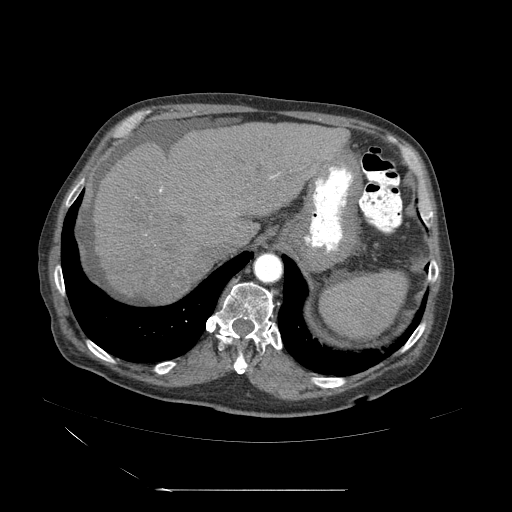
Contrast-enhanced abdominal CT (liver protocol), one axial slice. Slice 42 of 71 in the series (ordered by position). Reconstruction kernel STANDARD. 120 kVp. Soft-tissue window (W 400 / L 40 HU). 512 × 512 image matrix, field of view 440 × 440 mm. From the clinical record (not read from this slice): diagnosis: hepatocellular carcinoma (patient treated with transarterial chemoembolisation; whether this scan precedes or follows treatment is not stated here); TNM stage (as recorded): Stage-II; Child-Pugh class: A; tumour nodularity: multinodular; tumour size: 1 cm.
Outlined on this slice (semi-automatically segmented with operator editing):
- abdominal aorta: bounding box <254,255,284,285> (left, top, right, bottom; pixels)
- liver parenchyma outside the tumour (the mass and vessels are separate outlines, so this box may not span the whole liver): <88,124,351,309>
- mass: <150,268,189,308>
- liver vessels: <120,199,230,266>